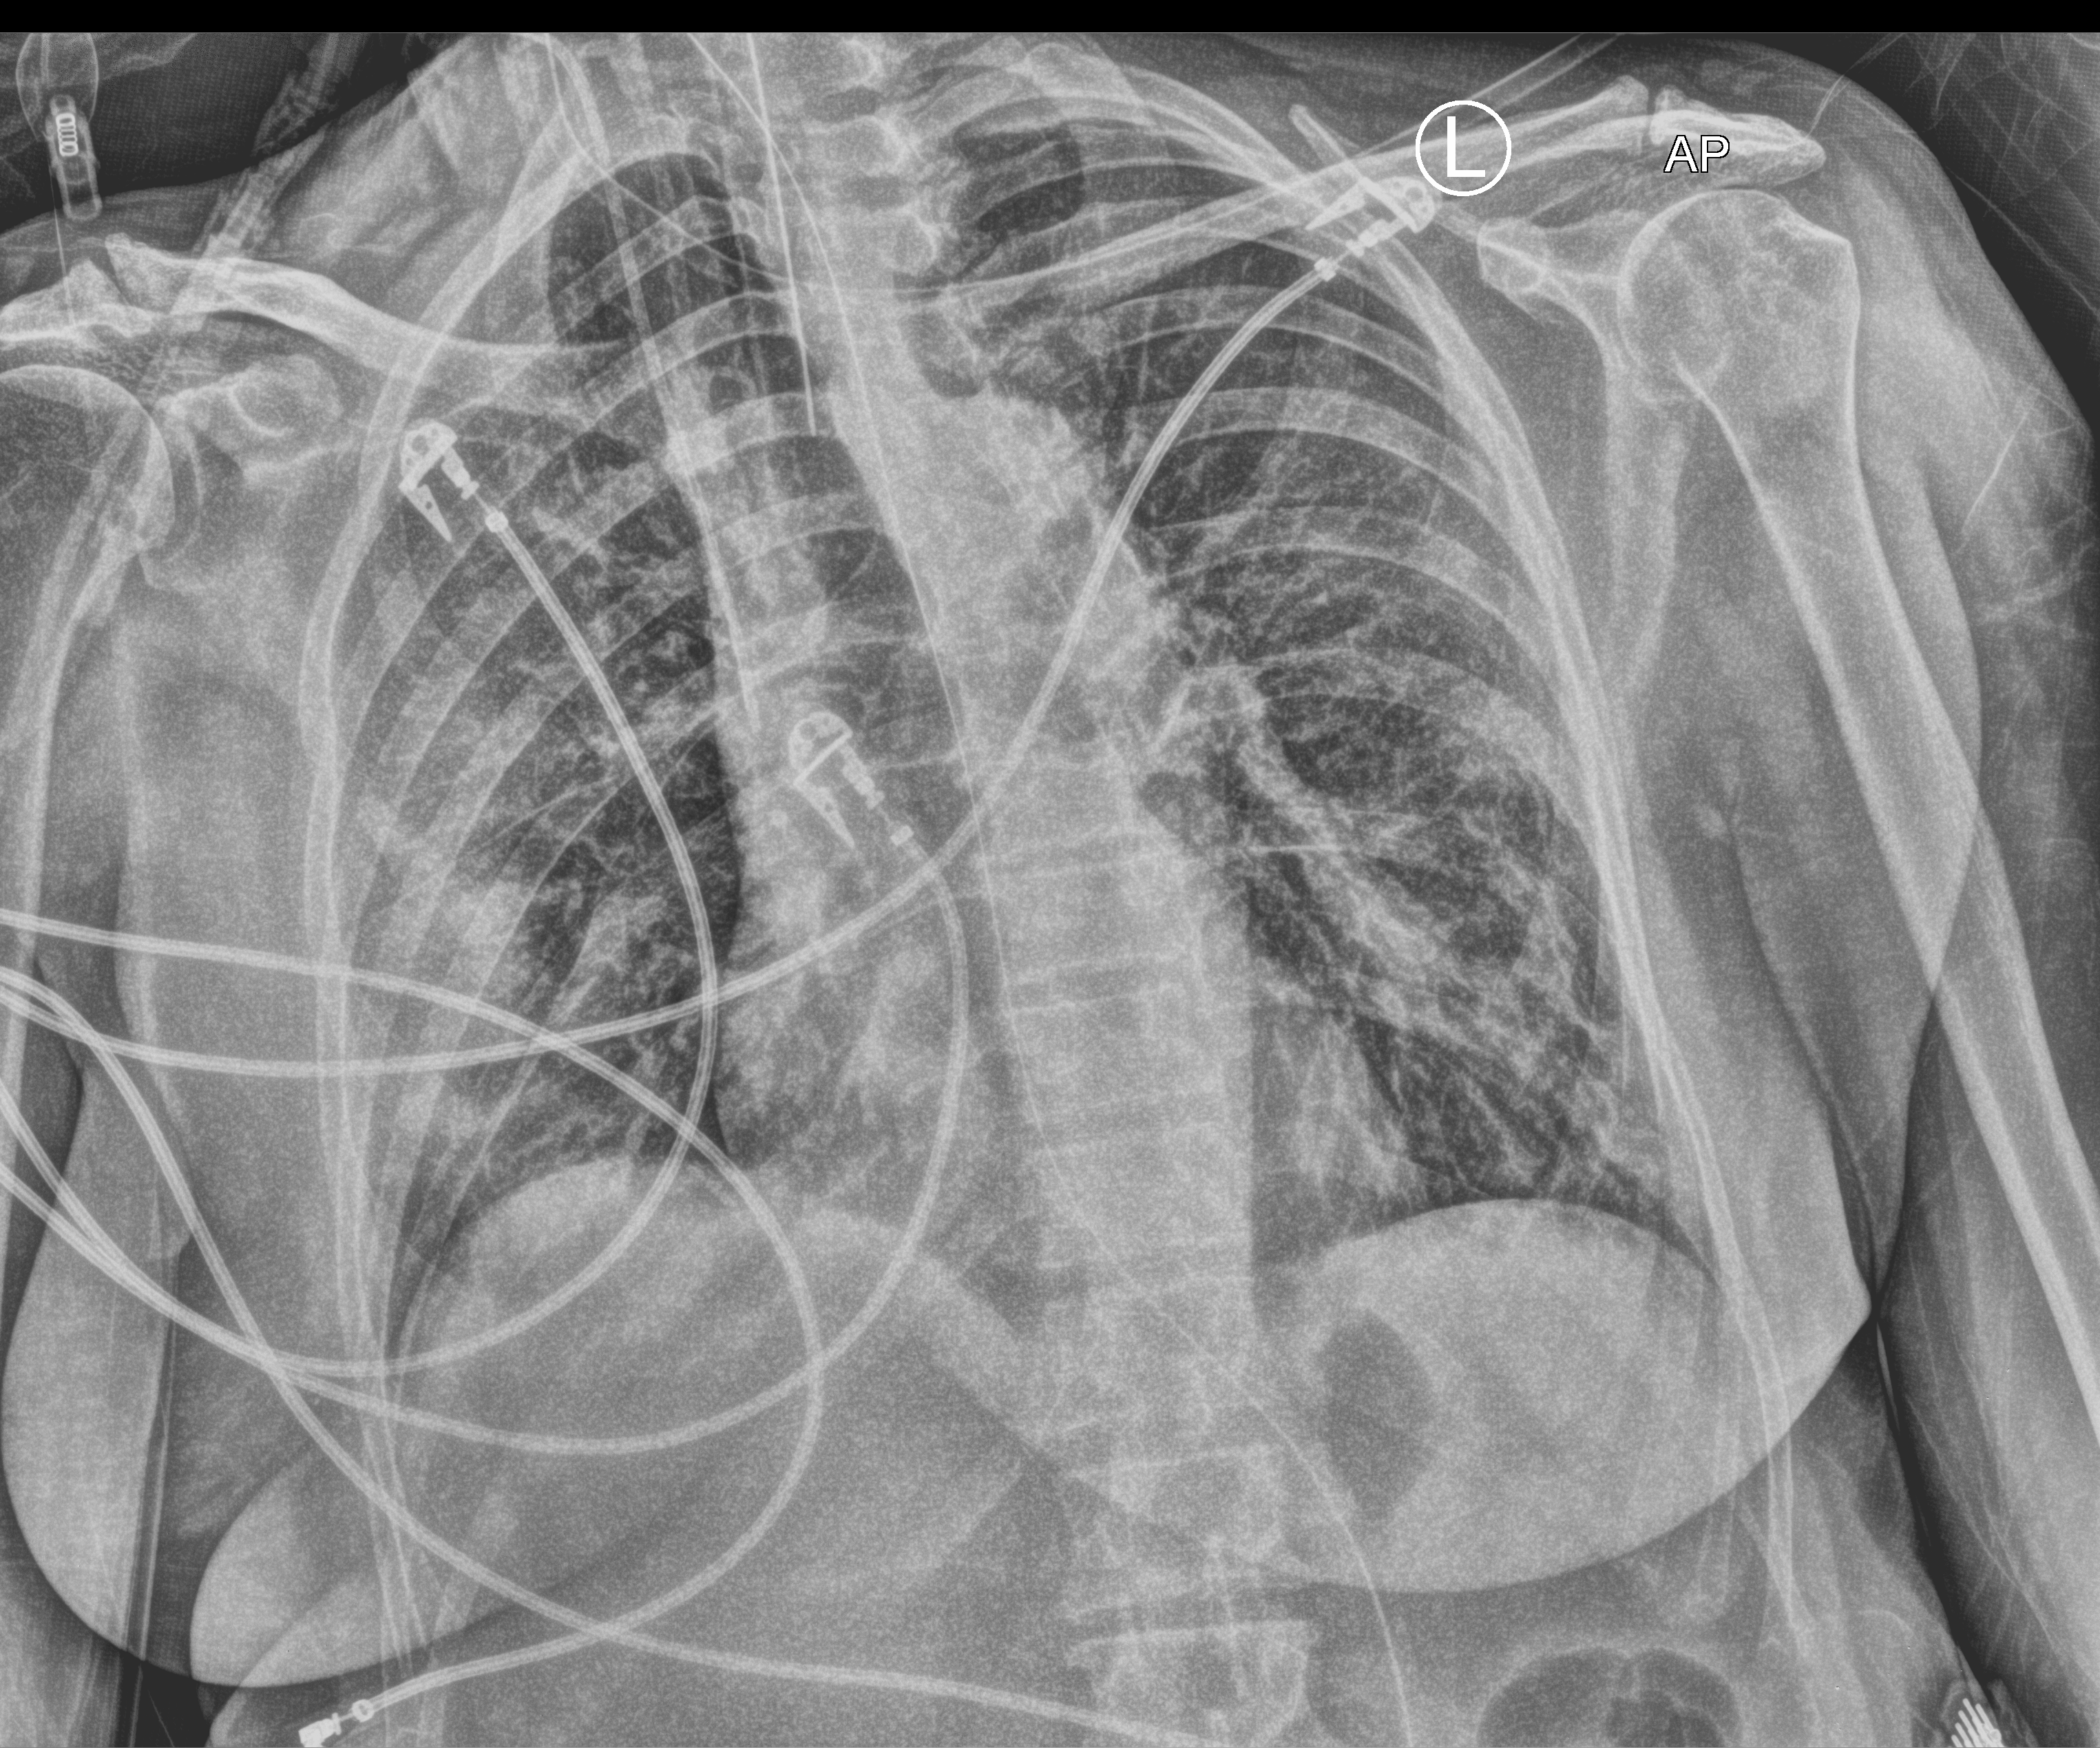
Portable chest radiograph; anteroposterior (AP) projection. Patient hospitalised with COVID-19; female, aged 60–74 years.
Admission-level facts for this patient (not findings on this image; timing relative to this image not recorded):
- length of hospital stay: 18 days
- mechanically ventilated during this hospital stay: yes